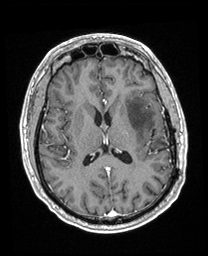
Brain MRI from a brain-tumour surgery series, one axial slice; slice 100 of 208 in the series (ordered by position); T1-weighted post-contrast; 1 mm slice thickness; 208 × 256 image matrix, field of view 211 × 260 mm. From the clinical record (not read from this slice): histopathology: Astrocytoma; WHO grade: 3; IDH mutation: yes; tumour location: Left Insular.
Annotated regions visible in this slice (manually delineated by an expert):
- previous resection cavity: bounding box <151,129,156,138> (left, top, right, bottom; pixels)